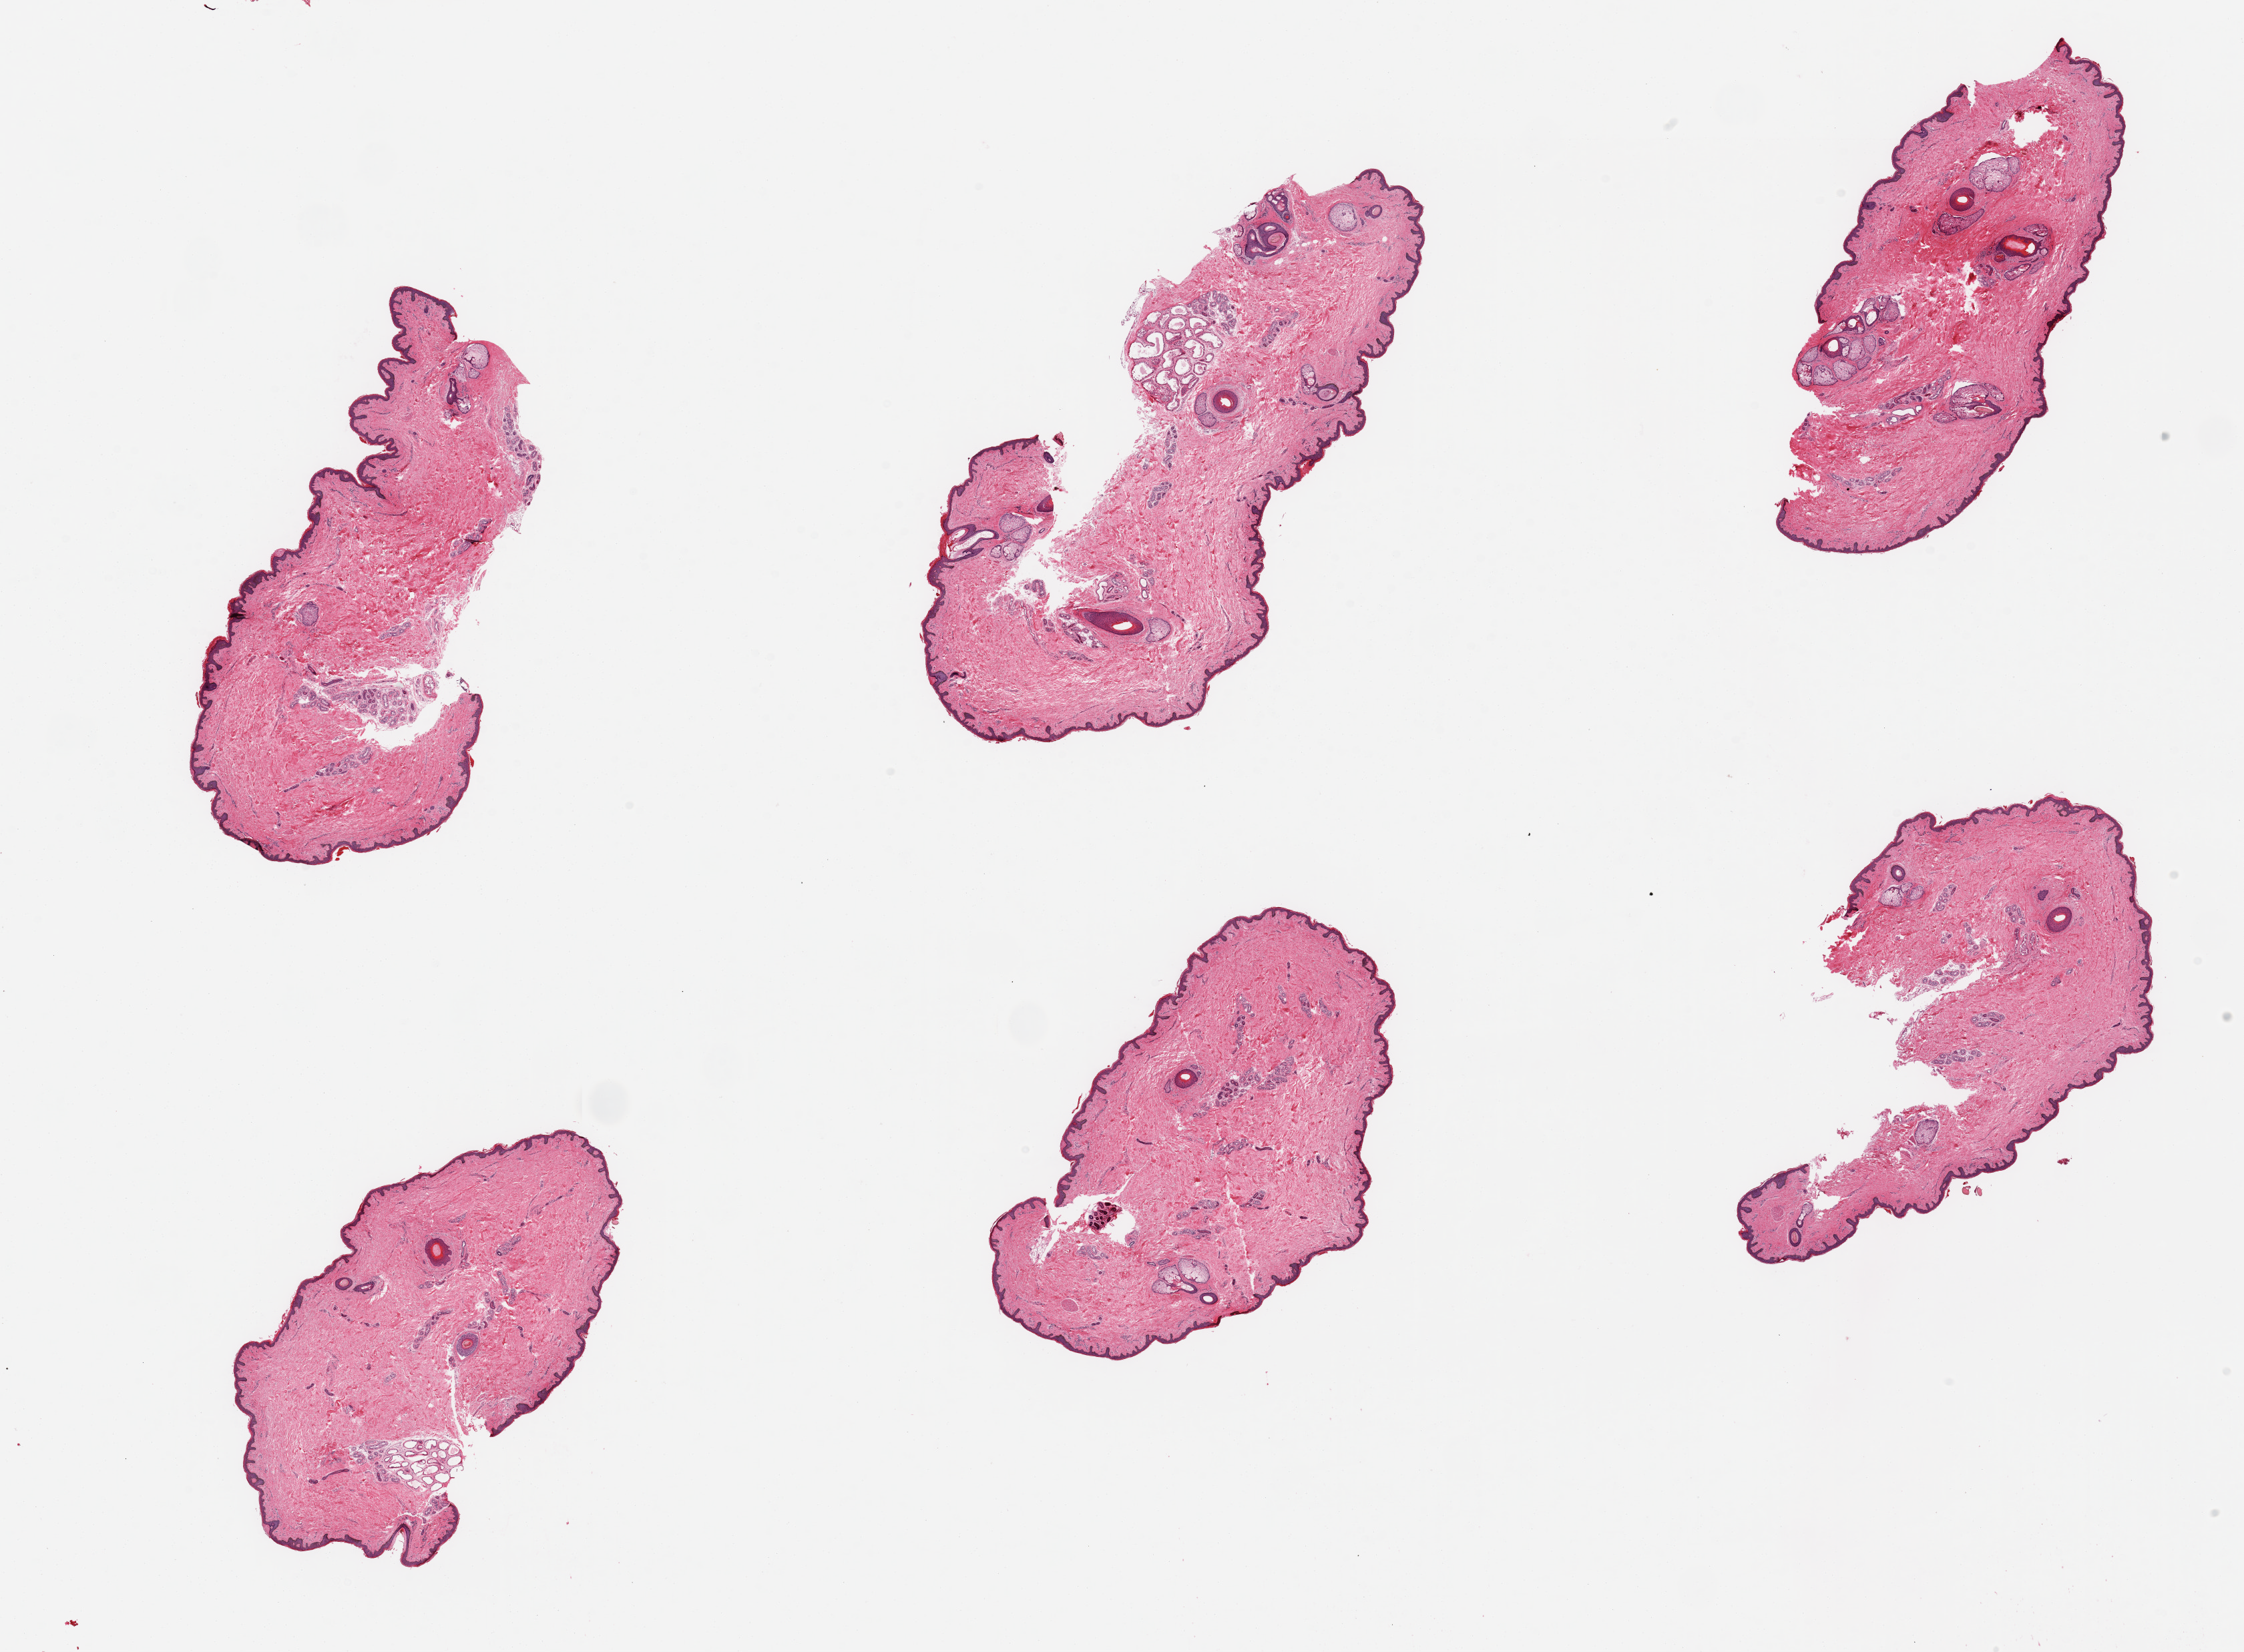
Hematoxylin and eosin (H&E) whole-slide image — whole scanned area (about 26.6 x 19.6 mm, slide scanned at 20x) shown as a low-resolution overview. PAXgene-fixed, paraffin-embedded tissue. Target tissue: skin of suprapubic region. Tissue donor sample. Donor: male.
• reviewer comment on this tissue sample: 6 pieces, minimal dermal fat; prominent adnexal glands noted (apocrine and eccrine); Squamous epithelium is ~40-45 microns